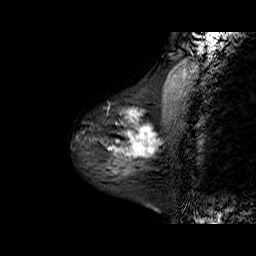
Breast MRI (dynamic contrast-enhanced), one sagittal slice. Position 15 of 60 along the scan axis. Dynamic contrast-enhanced series, time point 2 of 6 at this slice position (early post-contrast). 1.5 T. TE 6.3 ms, TR 32.9 ms. 256 × 256 image matrix. Female patient. Case-level facts recorded for this patient, not image findings: setting: breast cancer imaged before/during neoadjuvant chemotherapy; receptor status: HR-positive, HER2-negative.
Annotated regions visible in this slice (semi-automatic segmentation, software-assisted and operator-edited):
- analysis volume of interest (the breast-tissue region the enhancement analysis was run in; not a lesion): bounding box (x1, y1, x2, y2) in pixels: (89, 86, 169, 170)
- tumour enhancement mask (voxels above the 100 % enhancement threshold inside the analysis volume of interest): (133, 131, 149, 153)